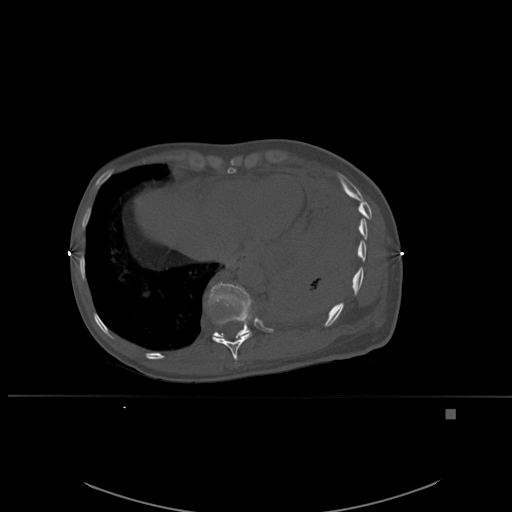
CT including the spine, one axial slice. Position 311 of 537 along the scan axis. Bone window (W 1800 / L 400 HU). 1.5 mm slice thickness. 512 × 512 image matrix, field of view 440 × 440 mm. Patient: female, 45 years. Case-level facts recorded for this patient, not image findings: primary cancer: lung.
Outlined on this slice (semi-automatic segmentation, software-assisted and operator-edited):
- T10 vertebra: bounding box (x1, y1, x2, y2) in pixels: (212, 332, 252, 364)
- T11 vertebra: (208, 282, 253, 338)